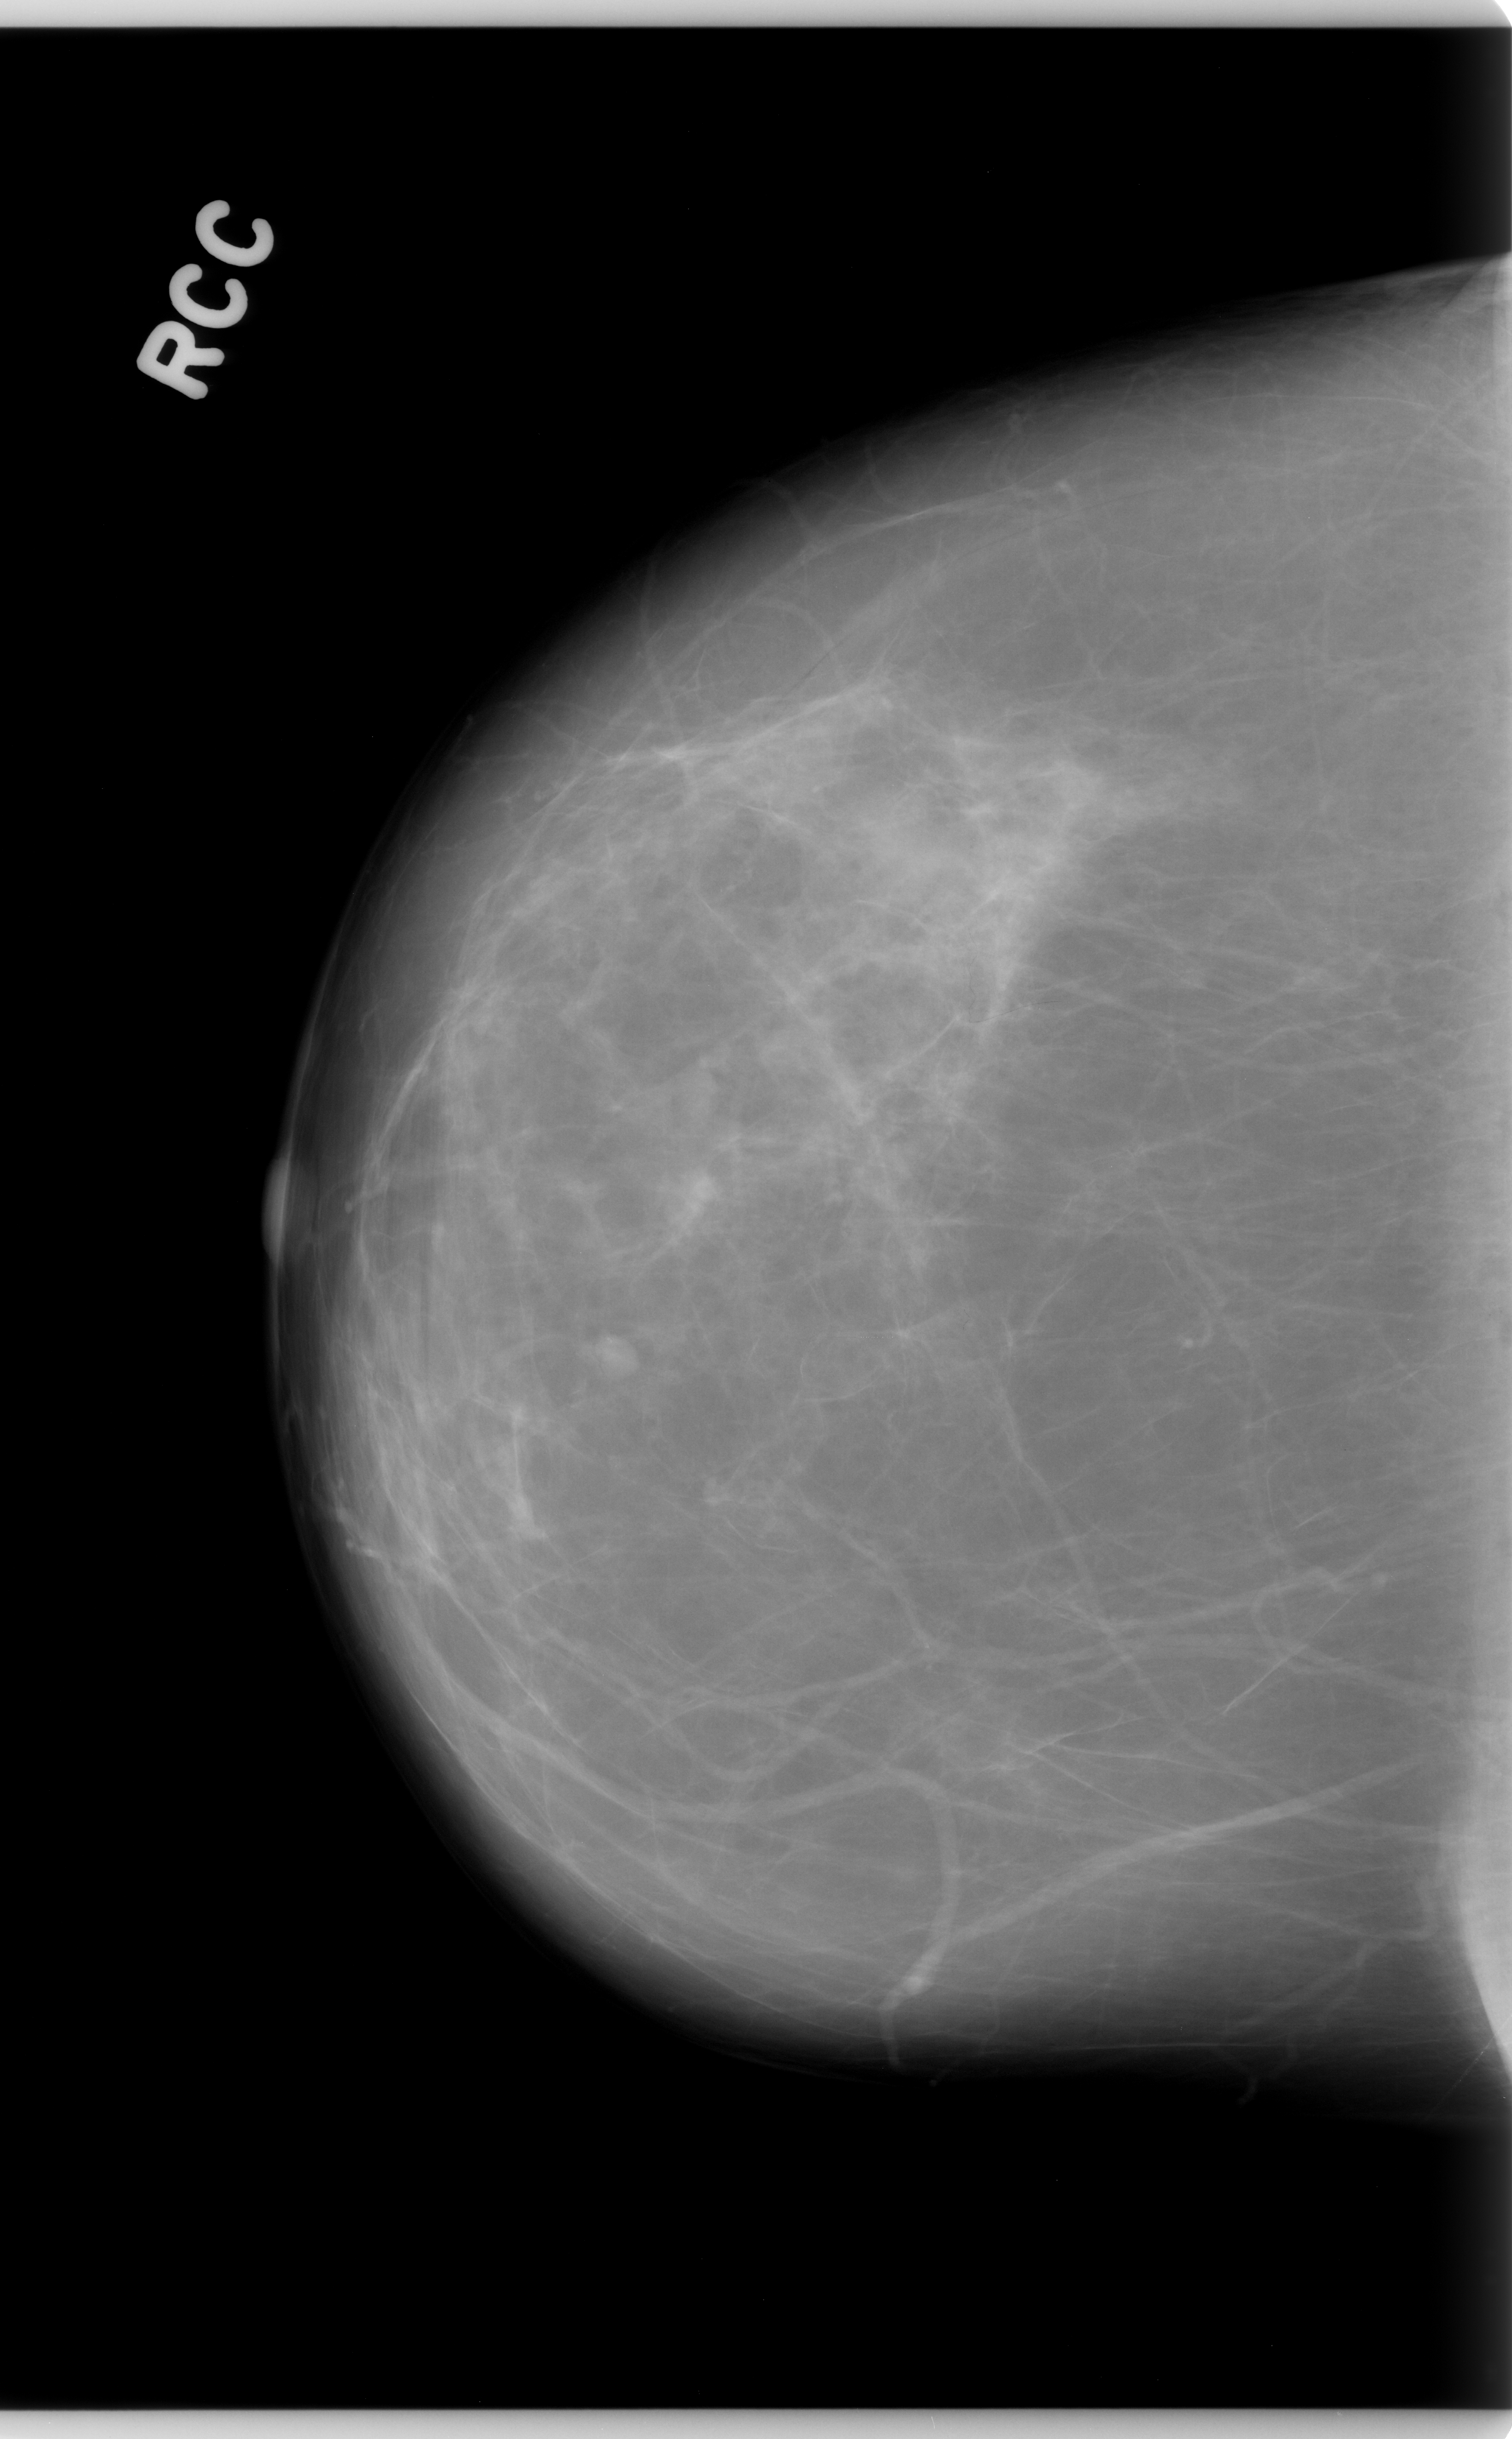
Mammogram (digitized film), right breast, craniocaudal (CC) view, breast composition: almost entirely fatty (BI-RADS density category 1 of 4).
Finding: calcifications, morphology punctate, distribution clustered; BI-RADS assessment category 4; subtlety rating 5 on a 1 (subtle) to 5 (obvious) scale; pathology result (as recorded, not read from the image): benign.